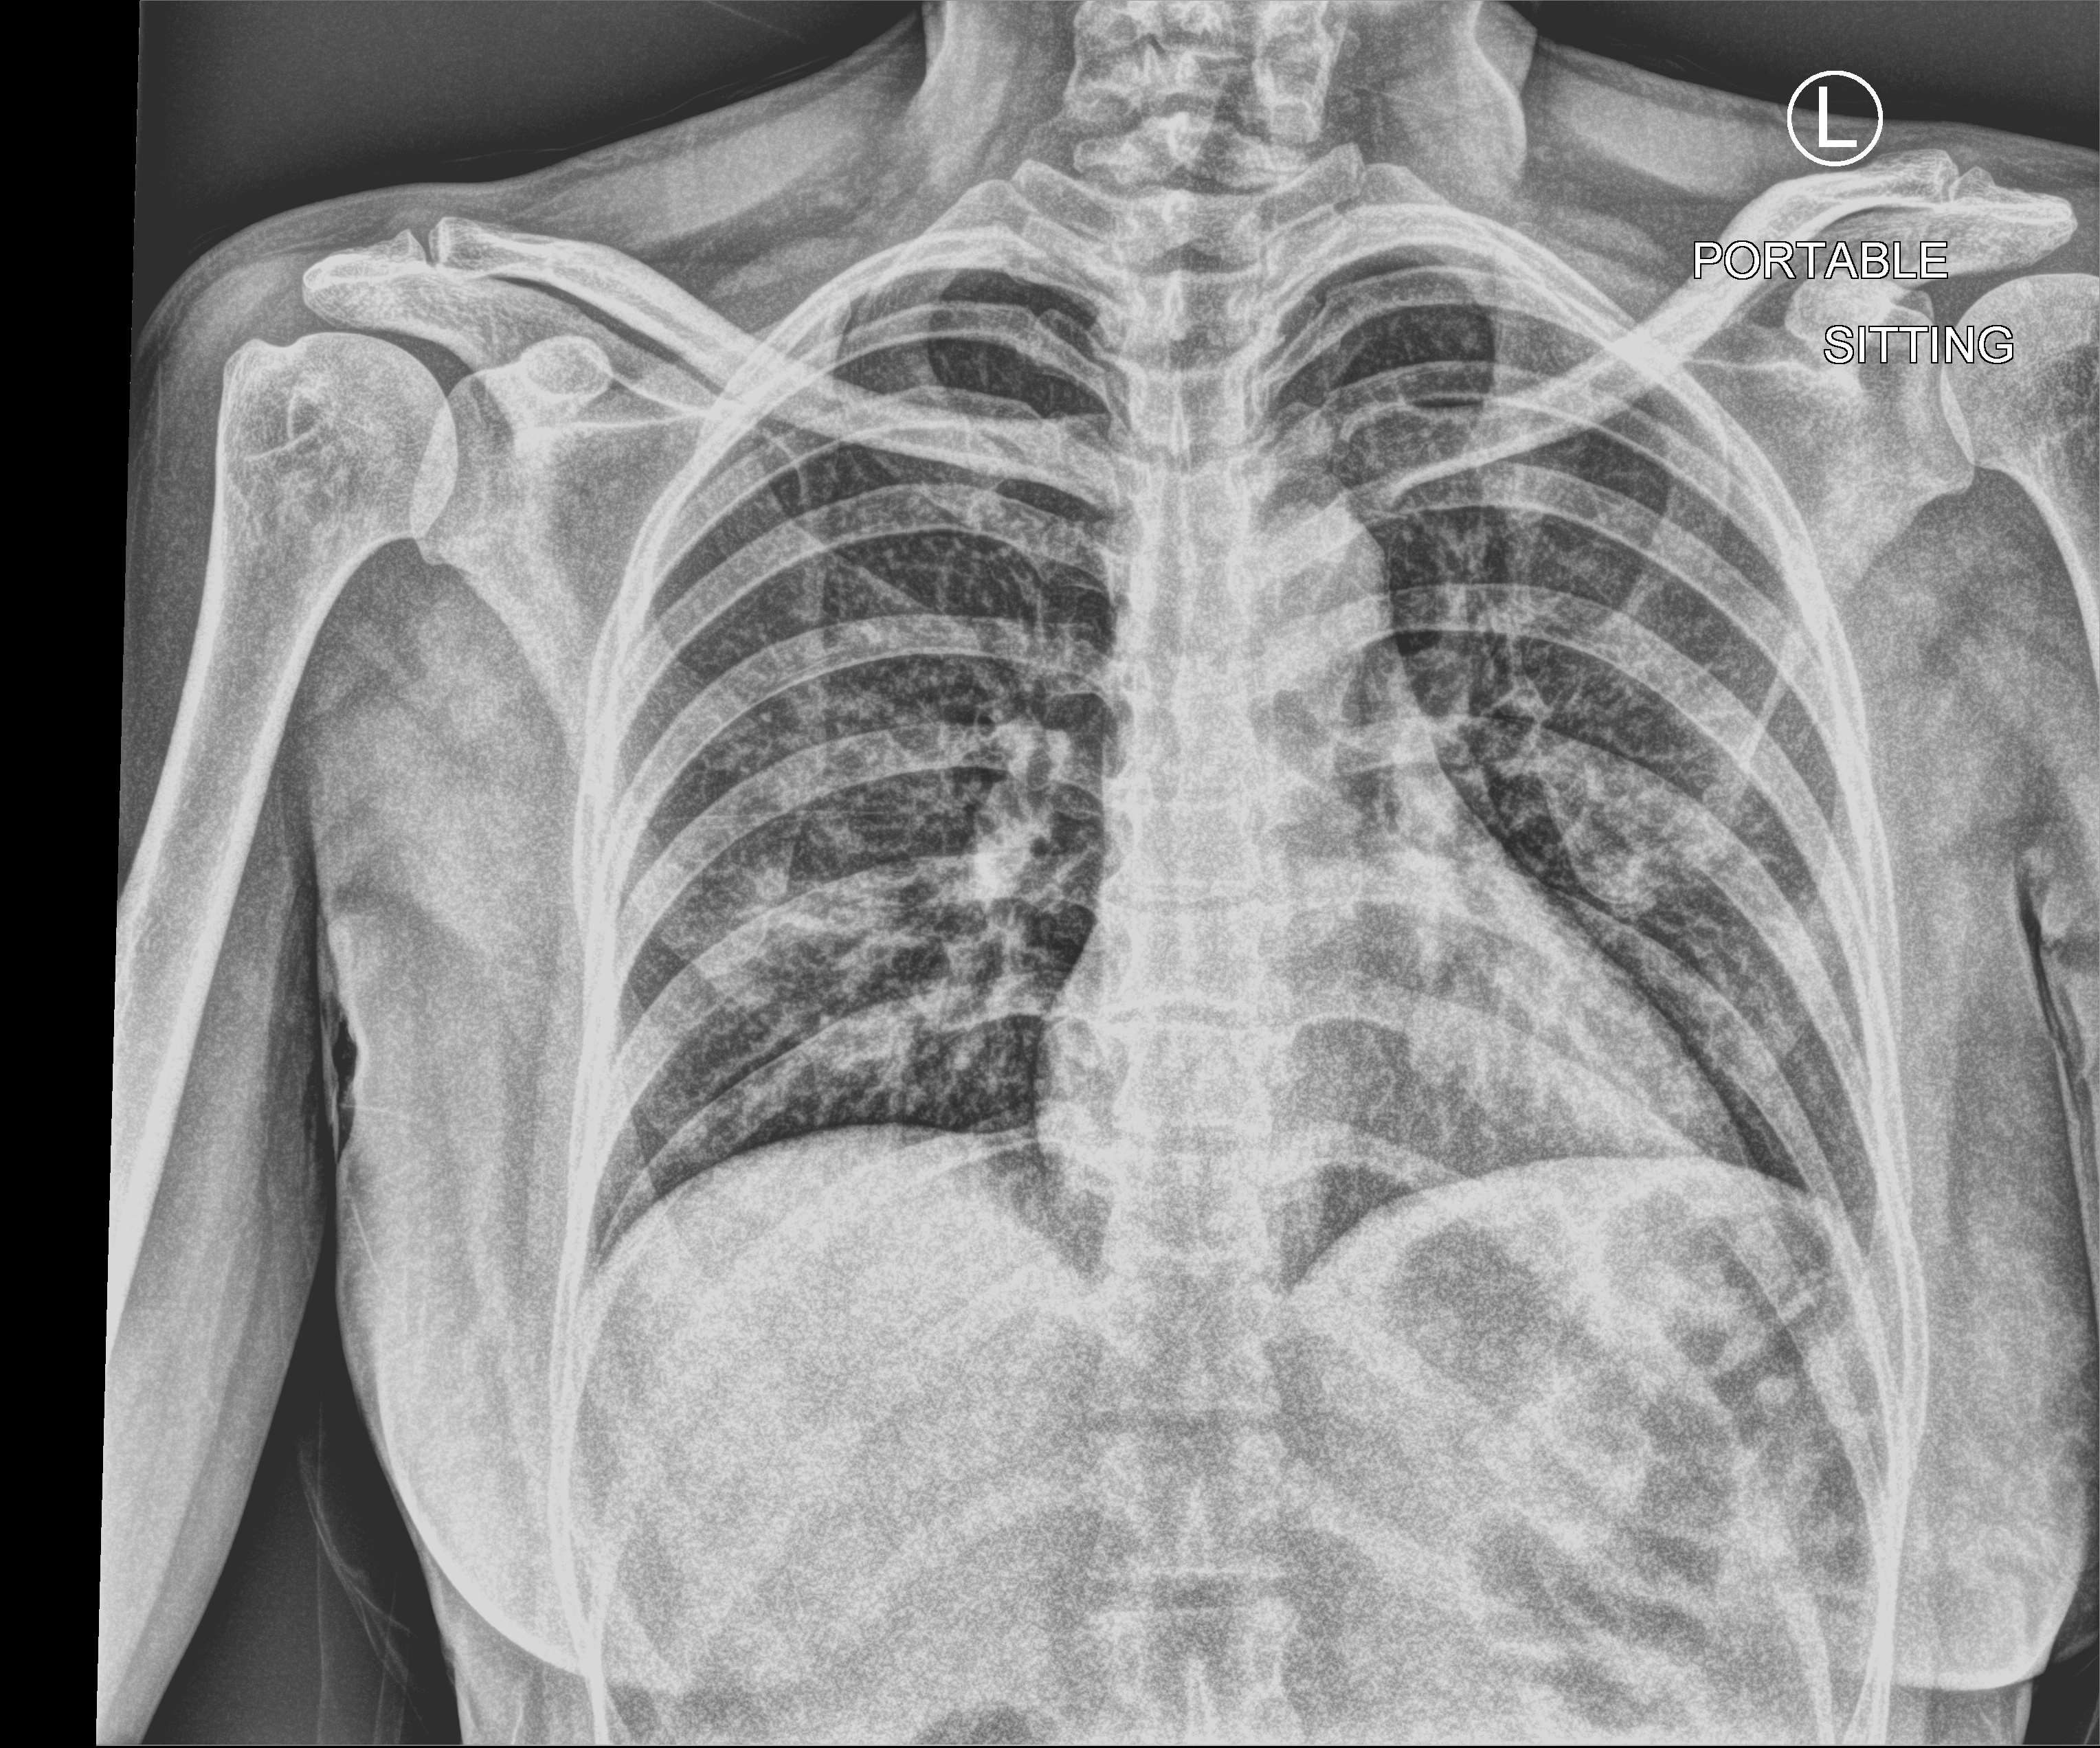
Portable chest radiograph, anteroposterior (AP) projection. Female patient hospitalised with COVID-19, age 18–59 years.
Hospital-stay facts (about this admission, not read from this image; timing relative to this image not recorded):
- mechanically ventilated during this hospital stay: no